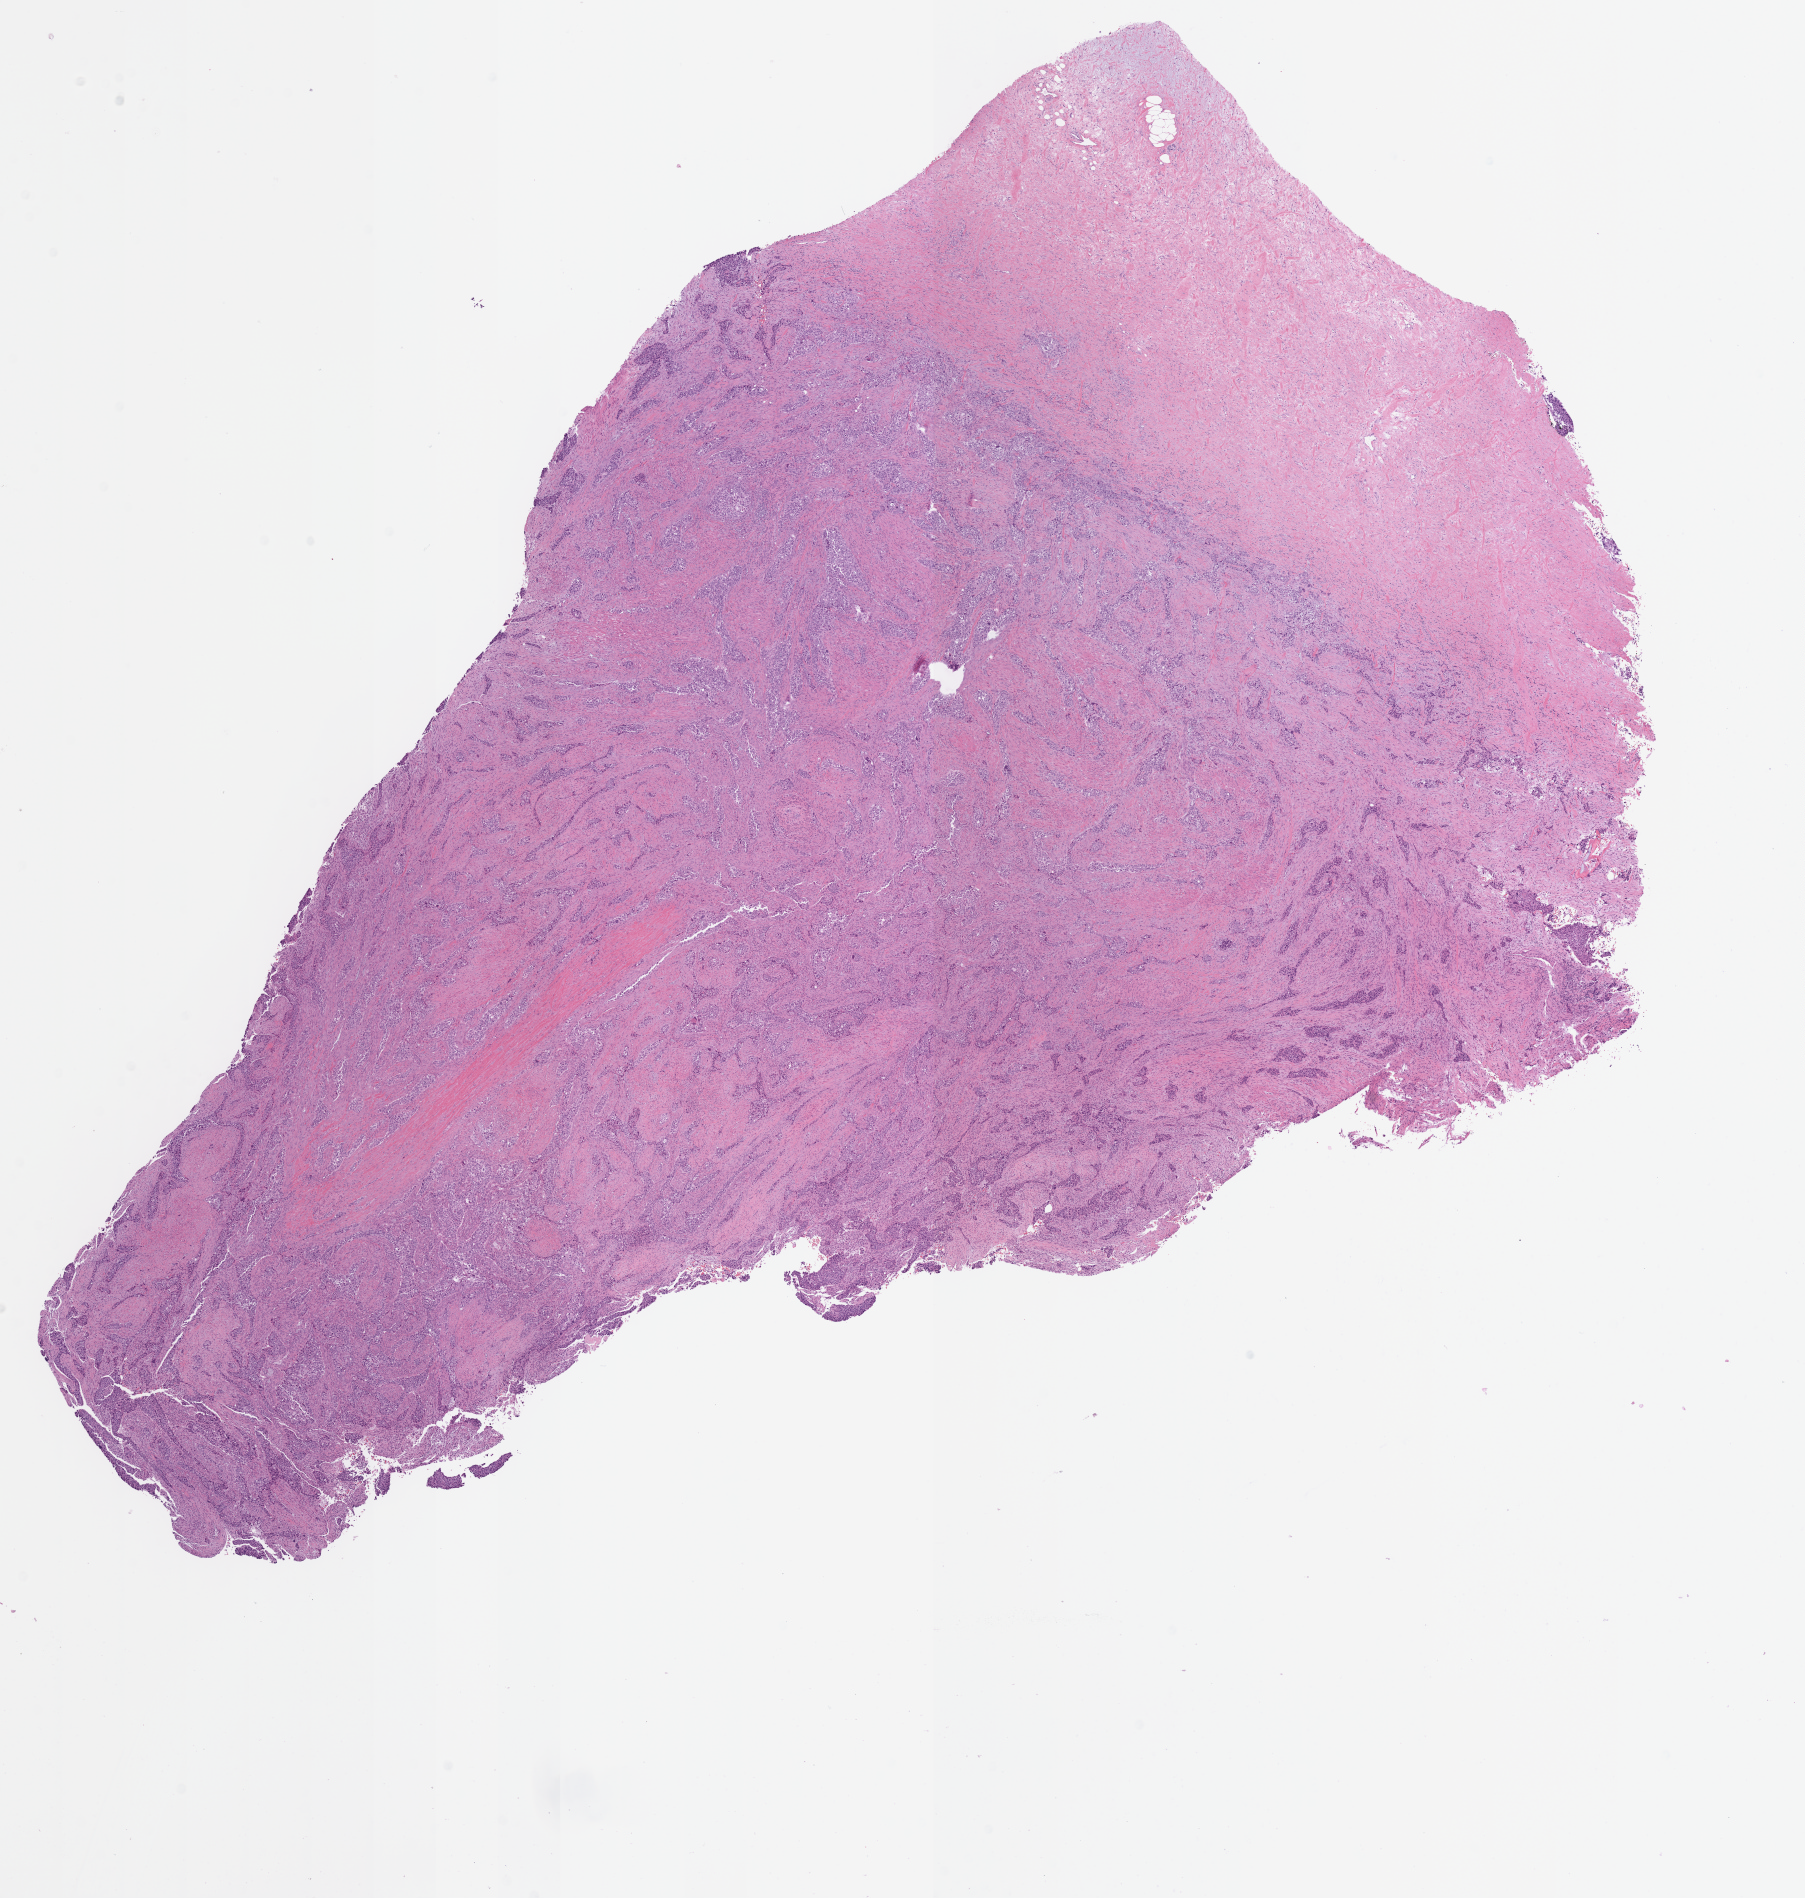
H&E-stained whole-slide image, low-resolution overview of the scanned area, about 14.2 x 14.9 mm (acquisition: 40x scan). Formalin-fixed paraffin-embedded (FFPE) diagnostic section. Sample: primary tumour, bladder. Male, age 61 years at initial diagnosis. Histologic grade: high grade.
Diagnosis: Transitional cell carcinoma. AJCC pathologic stage: IV.